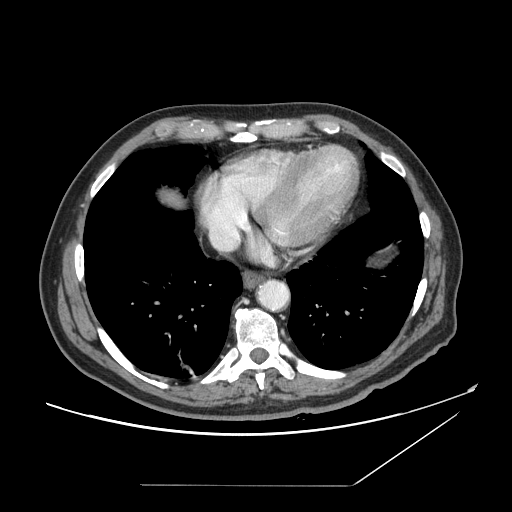
Contrast-enhanced abdominal CT, one axial slice; slice 147 of 166 in the series (ordered by position); intravenous contrast given; soft-tissue window (W 400 / L 40 HU); 512 × 512 image matrix, field of view 416 × 416 mm. Male patient, age 80 years. From the clinical record (not read from this slice): diagnosis: colorectal cancer liver metastases, imaged before liver resection; multiple liver metastases: no; largest metastasis: 2.2 cm.
Structures marked on this image (outlined manually by an expert reader):
- liver: box from (x=159, y=190) to (x=186, y=209) px
- planned liver remnant (the part of the liver to remain after resection): (x=158, y=189)–(x=186, y=209)